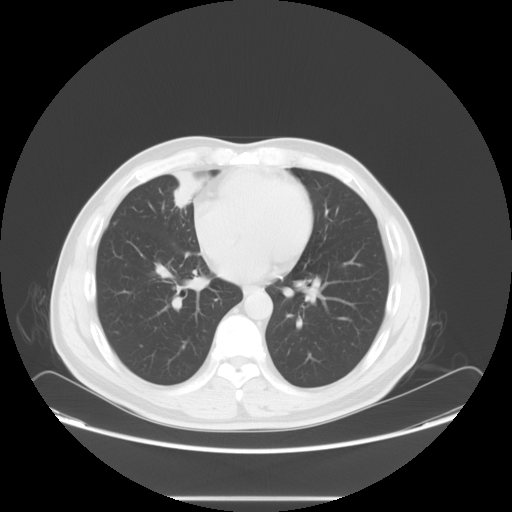
Chest CT, one axial slice. Slice 34 of 73 in the series (ordered by position). 120 kVp. Lung window (W 1500 / L -600 HU). 5 mm slice thickness. 512 × 512 image matrix, field of view 429 × 429 mm. Patient: male, 47 years. Case-level facts recorded for this patient, not image findings: clinical TNM (as recorded): T1c N3 M0.
Outlined on this slice (bounding box drawn by a radiologist):
- lung tumour (recorded histology: adenocarcinoma): bounding box [x1, y1, x2, y2] px = [162, 166, 219, 214]